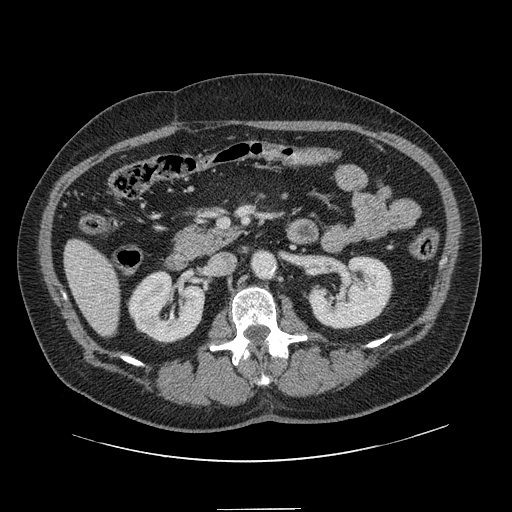
Contrast-enhanced abdominal CT, one axial slice; position 48 of 154 along the scan axis; 120 kVp; intravenous contrast given; soft-tissue window (W 400 / L 40 HU); 2.5 mm slice thickness; 512 × 512 image matrix, field of view 451 × 451 mm. Male patient, age 61 years. From the clinical record (not read from this slice): diagnosis: colorectal cancer liver metastases, imaged before liver resection; multiple liver metastases: yes; largest metastasis: 2.6 cm; disease in both lobes: yes.
Structures marked on this image (outlined manually by an expert reader):
- hepatic veins: box from (x=98, y=294) to (x=101, y=302) px
- liver: (x=66, y=240)–(x=120, y=336)
- planned liver remnant (the part of the liver to remain after resection): (x=66, y=241)–(x=120, y=336)